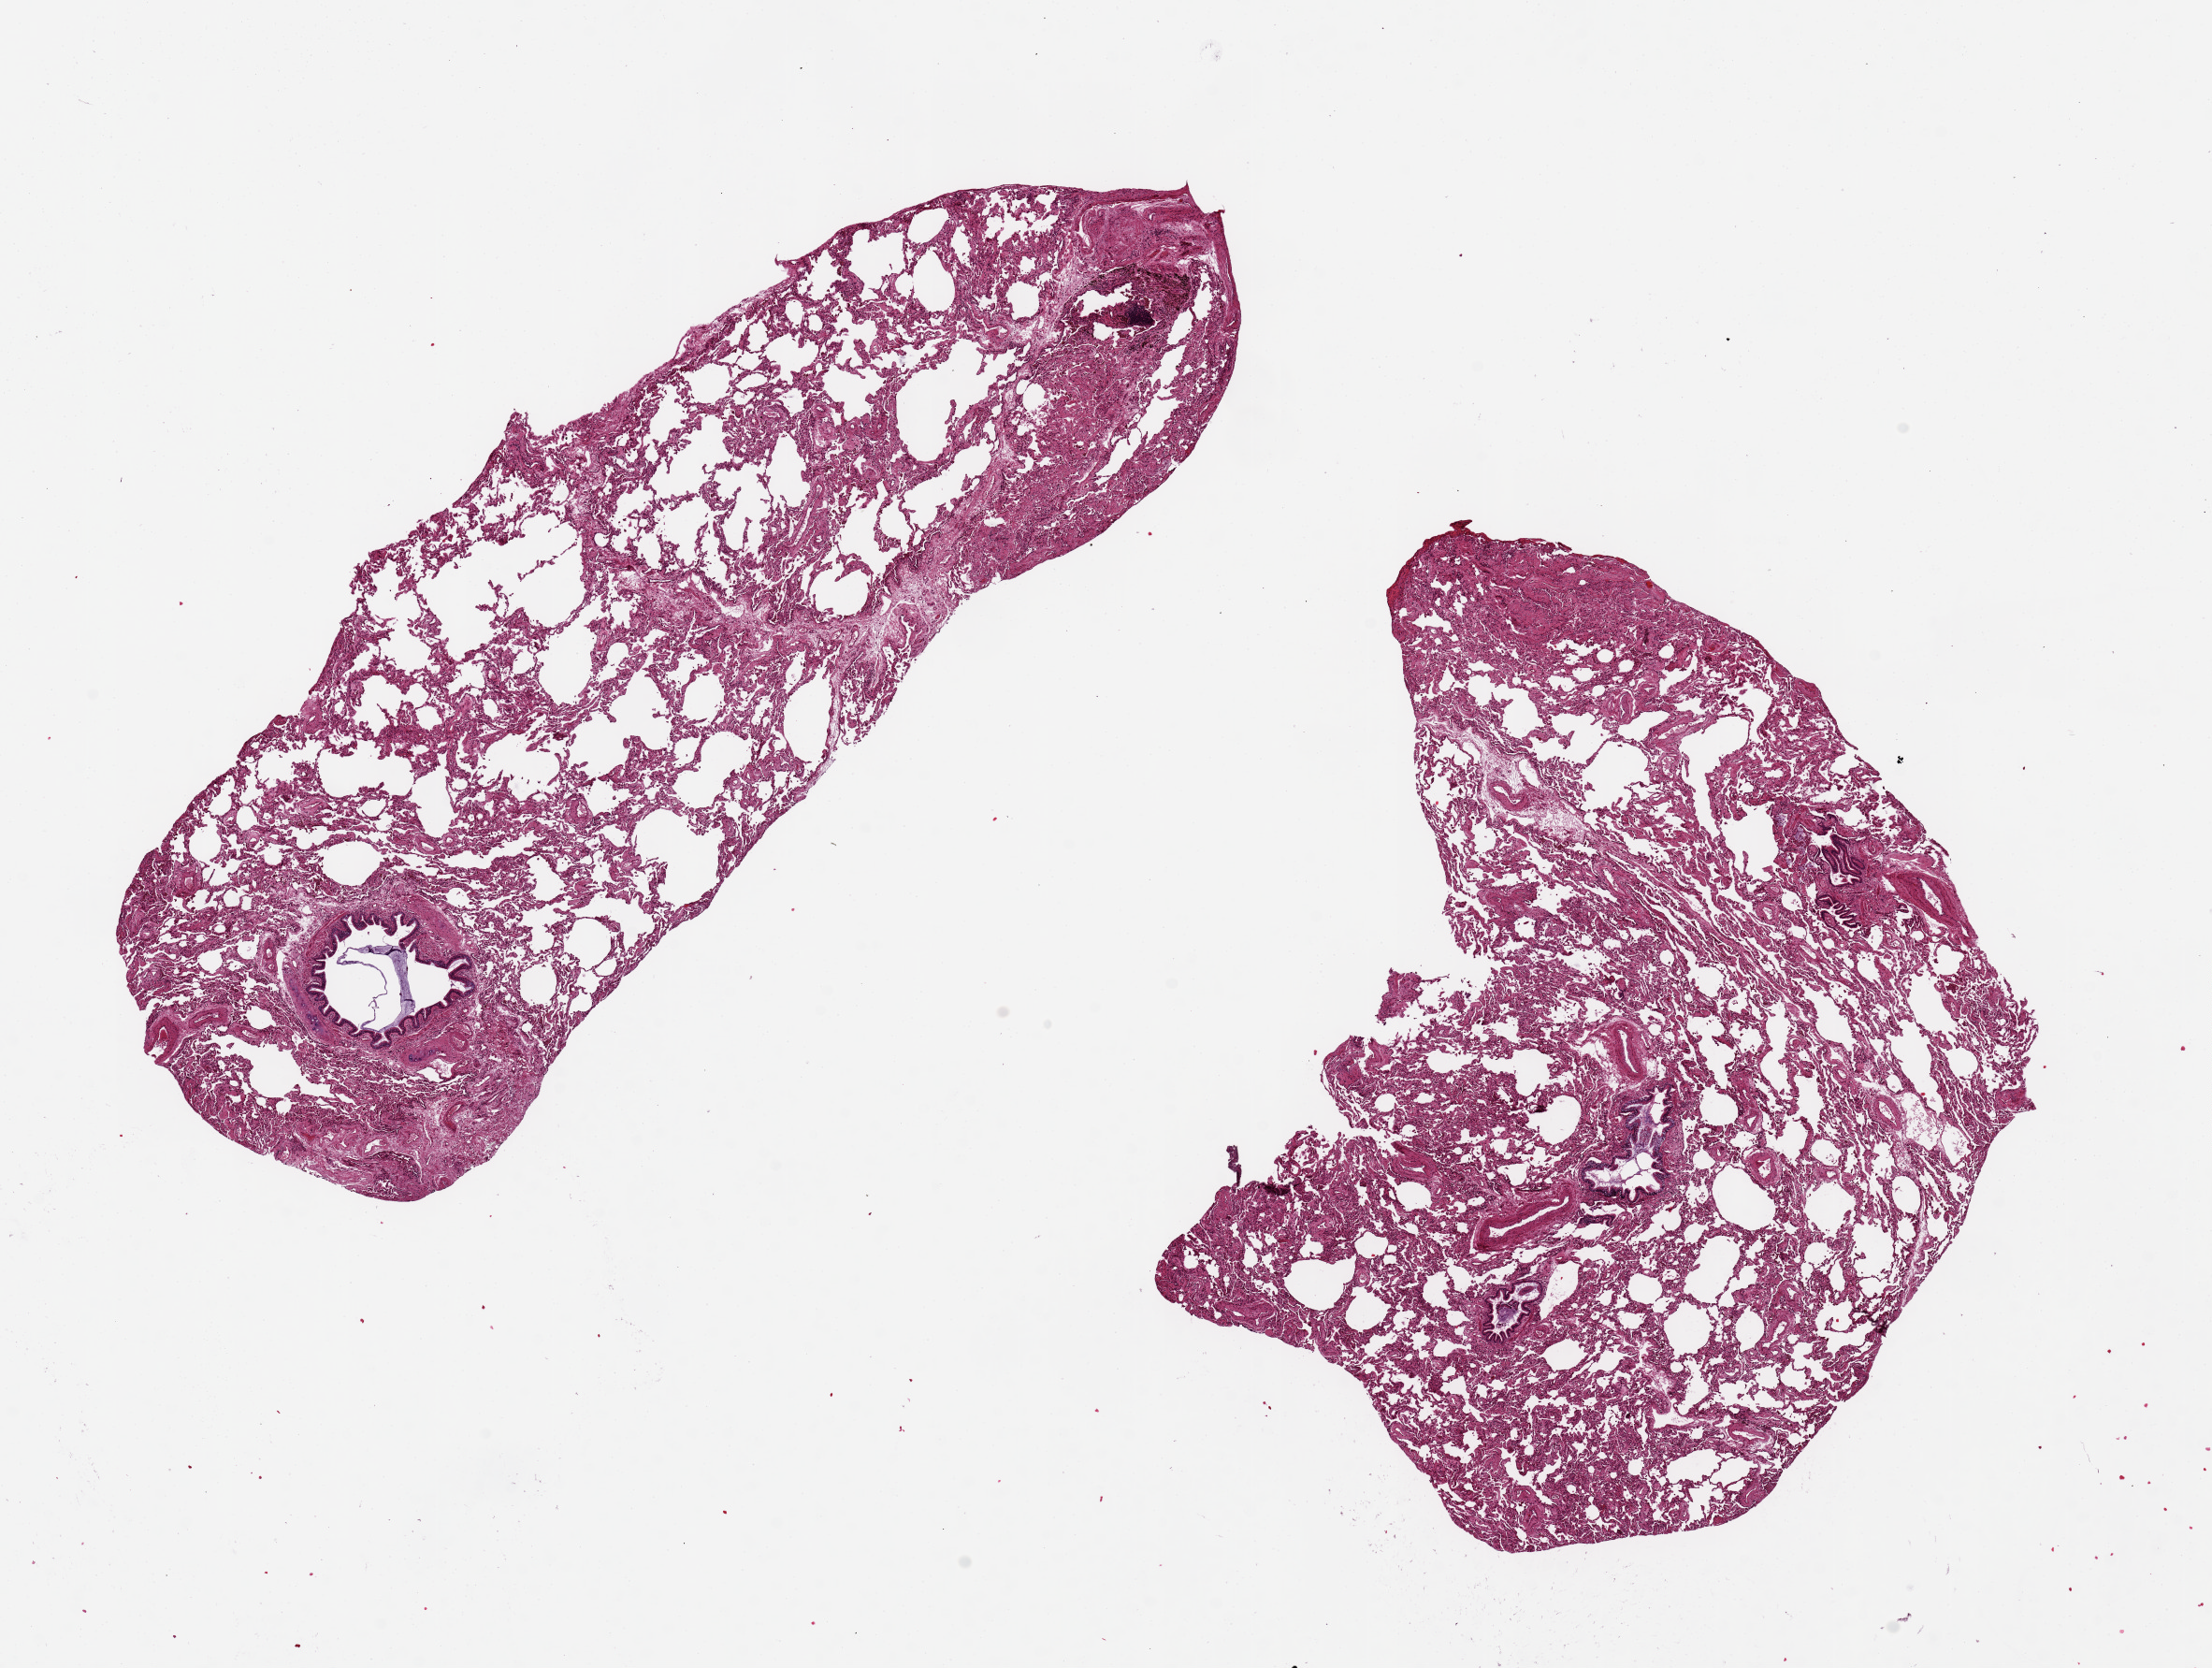
Digitized haematoxylin and eosin-stained section, brightfield — a low-resolution overview of the entire scanned area, about 18.7 x 14.1 mm, PAXgene-fixed paraffin-embedded (PFPE) section, sampled site (target tissue): lung, tissue donor sample. Male donor.
• reviewer comment on this tissue sample: 2 pieces 11x4 & 7x7 mm; patchy emphysema and fibrosis; no inflammation